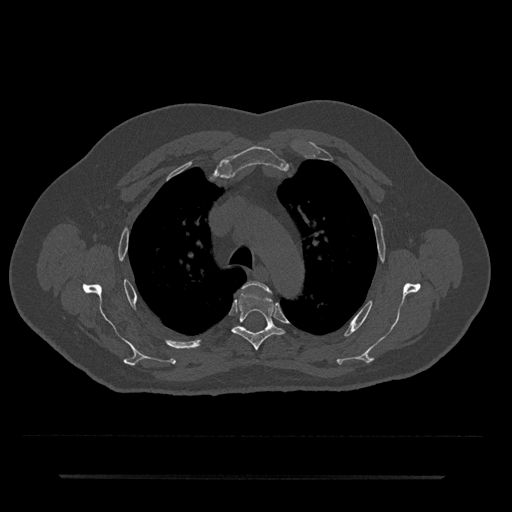
CT including the spine, one axial slice. Slice 529 of 797 in the series (ordered by position). Bone window (W 1800 / L 400 HU). 0.5 mm slice thickness. 512 × 512 image matrix, field of view 437 × 437 mm. Male patient, age 69 years. Case-level facts recorded for this patient, not image findings: primary cancer: prostate.
Outlined on this slice (semi-automatic segmentation, software-assisted and operator-edited):
- T3 vertebra: bounding box <242,281,270,293> (left, top, right, bottom; pixels)
- T4 vertebra: <233,292,285,350>